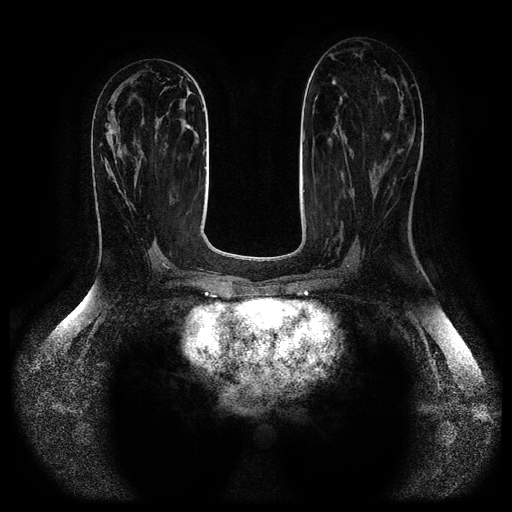
Breast MRI (dynamic contrast-enhanced, multi-phase), one axial slice; position 42 of 116 along the scan axis; dynamic contrast-enhanced series, time point 2 of 5 at this slice position (early post-contrast); 1.5 T; TE 2.6 ms, TR 5.2 ms; 512 × 512 image matrix, field of view 380 × 380 mm. Female patient, age 44 years.
Structures marked on this image (semi-automatic segmentation, software-assisted and operator-edited):
- breast lesion (labelled benign in the annotation): bounding box (x1, y1, x2, y2) in pixels: (383, 136, 388, 140)
- breast lesion (labelled benign in the annotation): (101, 129, 141, 206)